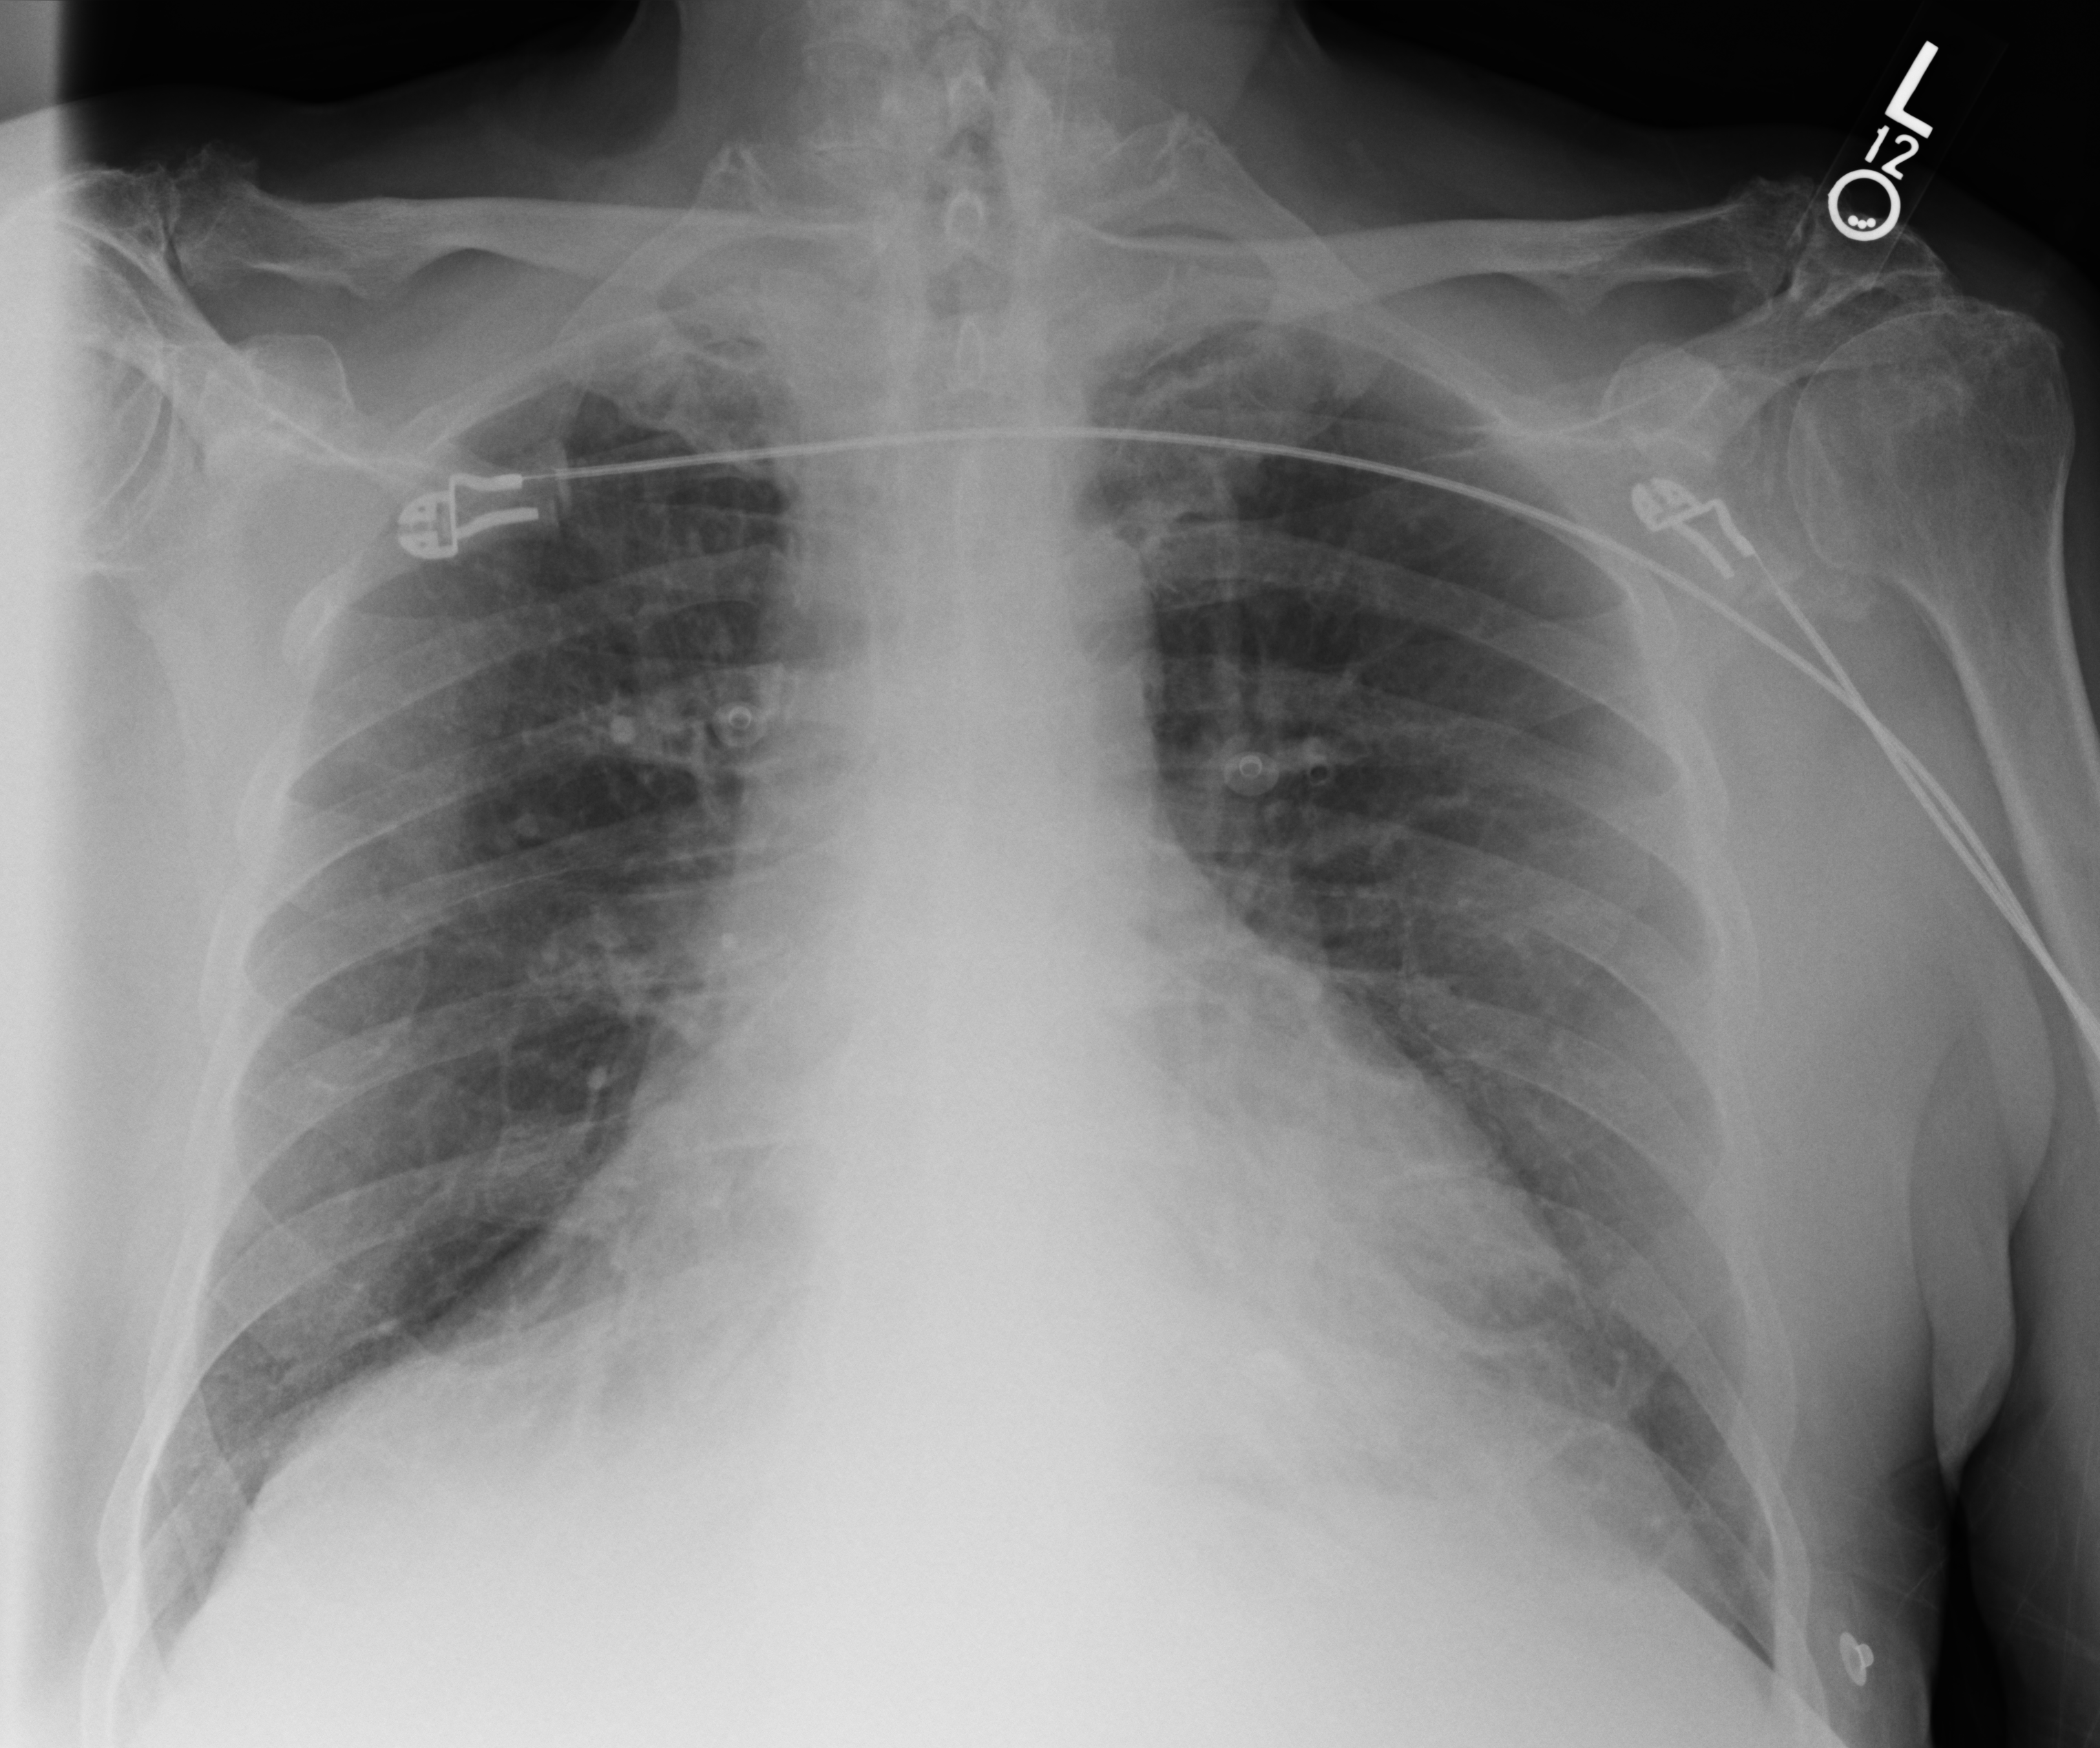
Portable chest radiograph; anteroposterior (AP) projection. Patient hospitalised with COVID-19; male, aged 75–90 years.
Hospital-stay facts (about this admission, not read from this image; timing relative to this image not recorded): mechanically ventilated during this hospital stay: no; length of hospital stay: 15 days; admitted to intensive care during this hospital stay: no.